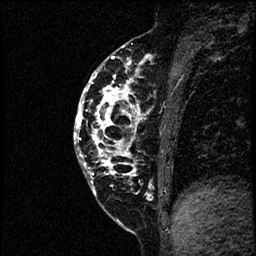
Breast MRI (dynamic contrast-enhanced), one sagittal slice. Position 27 of 60 along the scan axis. Dynamic contrast-enhanced study with each time point stored as its own series, time point 2 of 4 at this slice position (early post-contrast, ordered by acquisition time). 1.5 T. TE 4.2 ms, TR 17.6 ms. 2 mm slice thickness. 256 × 256 image matrix. Patient: female, 40 years. From the clinical record (not read from this slice): setting: breast cancer imaged before/during neoadjuvant chemotherapy; receptor status: HER2-positive.
Structures marked on this image (semi-automatic segmentation, software-assisted and operator-edited):
- analysis volume of interest (the breast-tissue region the enhancement analysis was run in; not a lesion): bounding box [x1, y1, x2, y2] px = [75, 56, 197, 205]
- tumour enhancement mask (voxels above the 100 % enhancement threshold inside the analysis volume of interest): [75, 56, 152, 197]